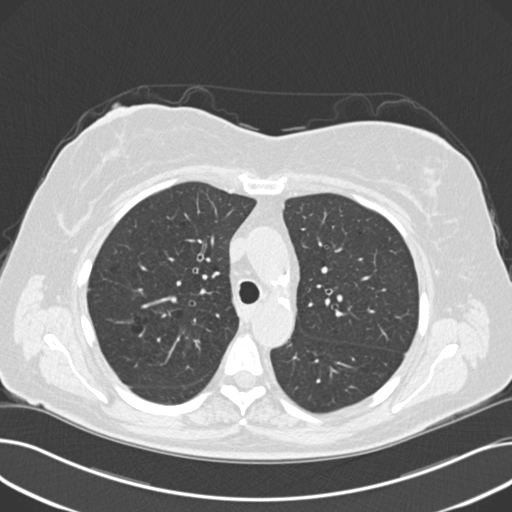
Low-dose screening chest CT, axial slice; third annual screen; lung window (W 1500 / L -600 HU); 2 mm slice thickness; 120 kVp; slice 69 of 203 in the series. Female participant, aged 60 years at enrolment. Current smoker at enrolment.
- Expert reader's lesion annotation, box from (x=311, y=227) to (x=363, y=270) px.
- The screening reader recorded 8 non-calcified nodules or masses ≥4 mm on this exam (right upper lobe, lingula, lingula, right middle lobe, right lower lobe, left lower lobe, left lower lobe, left lower lobe); which of them this box marks is not recorded.
- Official screen result: positive, other.
- Participant outcome: lung cancer diagnosed 176 days after this screen — non-small cell carcinoma, left upper lobe, poorly differentiated (G3), stage IB (AJCC 6th edition), 7 mm at pathology.